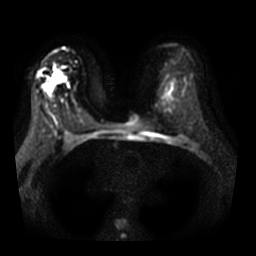
Breast MRI, one axial slice; slice 21 of 32 in the series (ordered by position); diffusion-weighted series; image 2 of 4 stored at this slice position (different b-values; order by instance number); 3 T; 5 mm slice thickness; 256 × 256 image matrix, field of view 350 × 350 mm. Female patient.
Structures marked on this image (expert manual segmentation):
- tumour on diffusion-weighted imaging: bounding box [x1, y1, x2, y2] px = [52, 73, 64, 85]